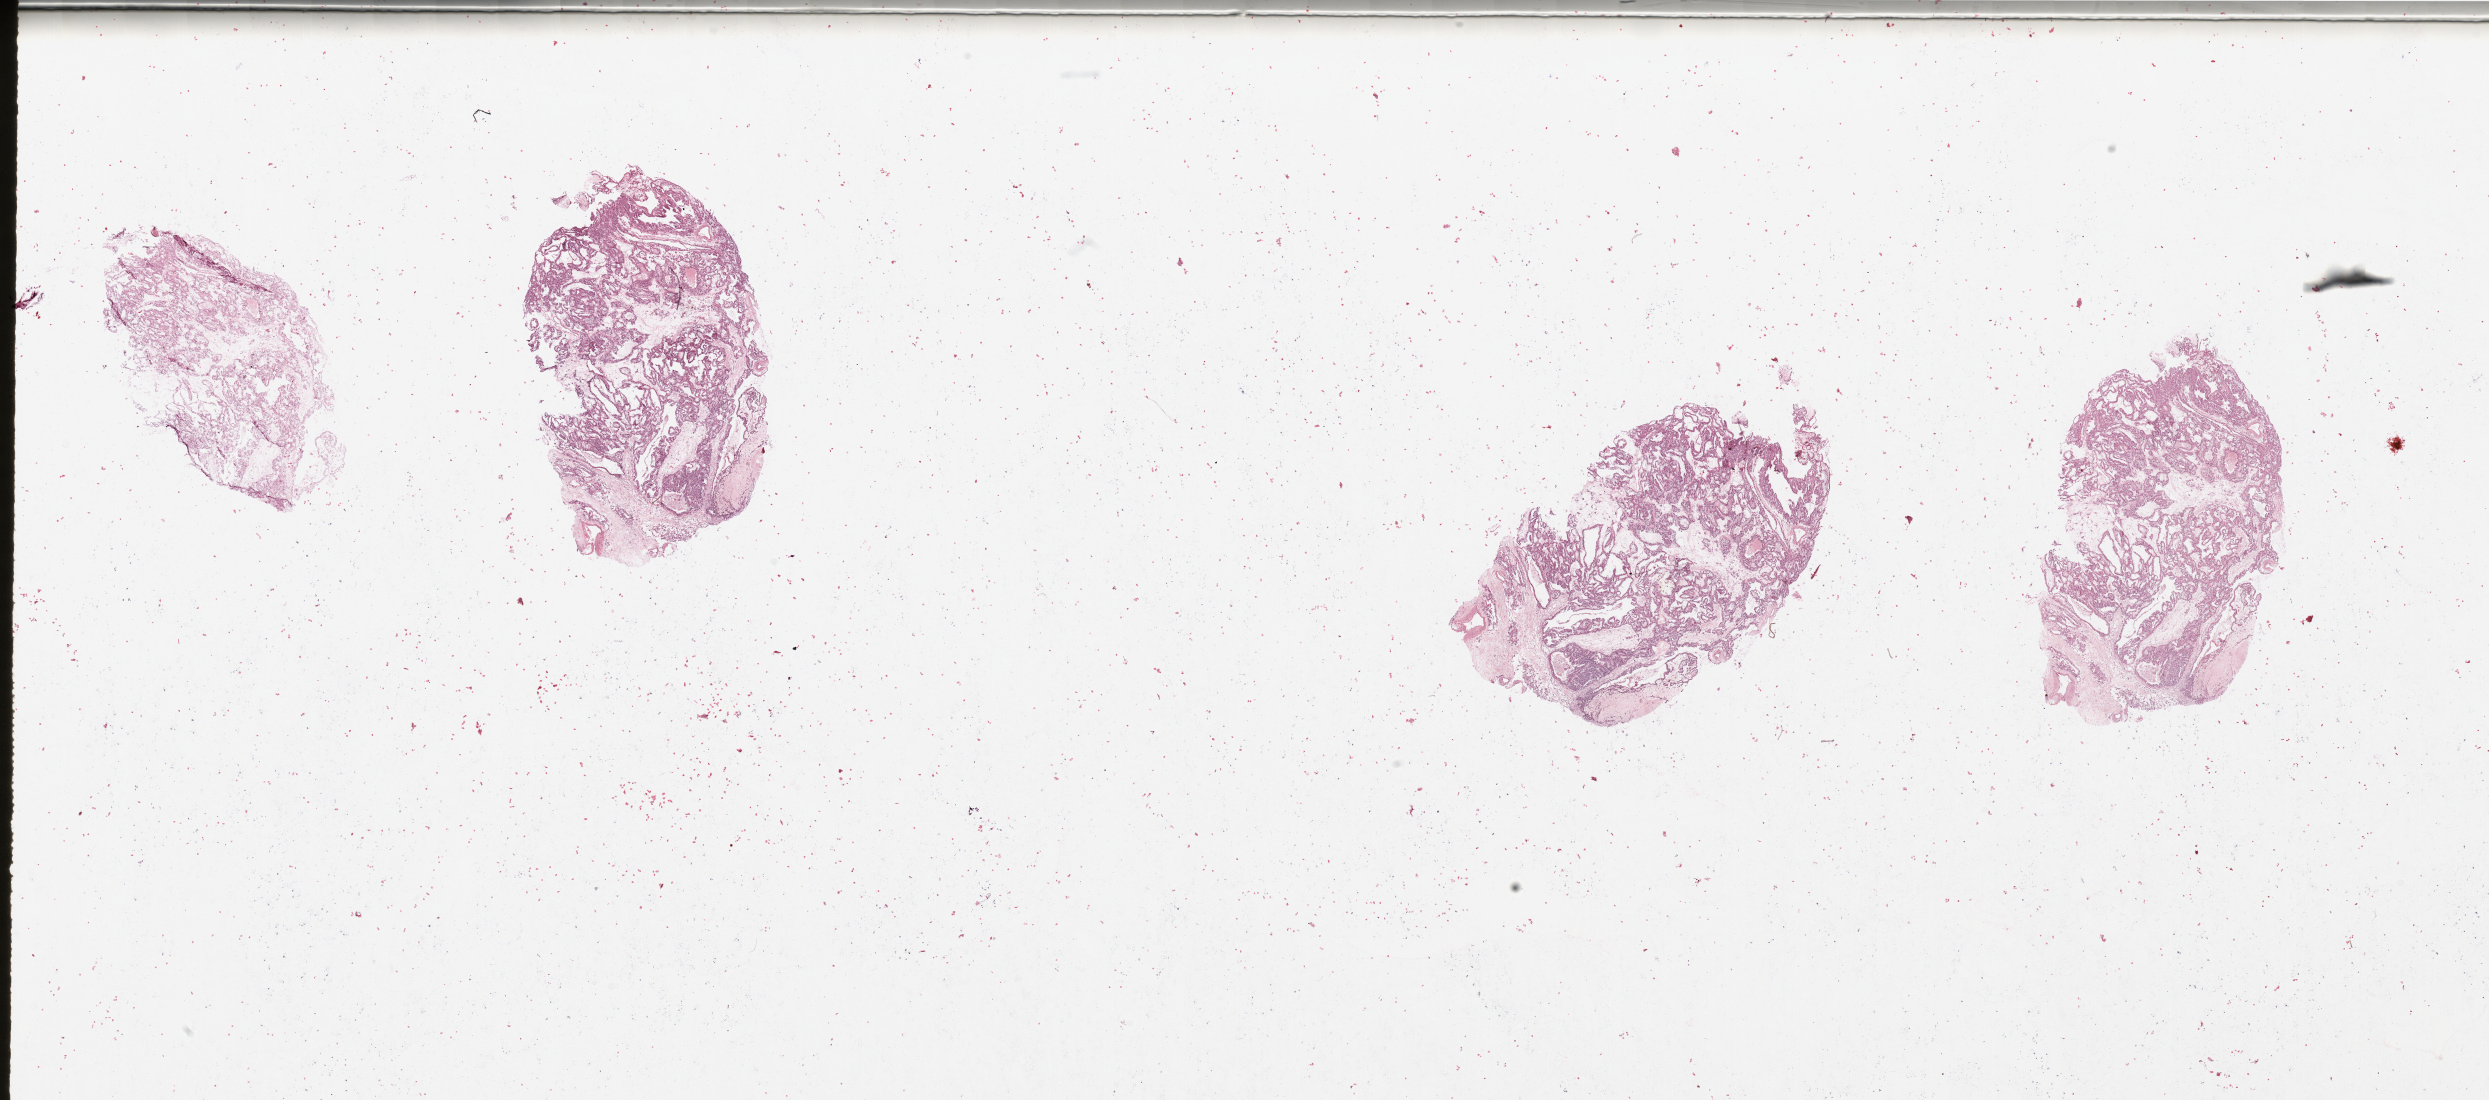
Digitized H&E-stained tissue section (whole slide), whole scanned area (about 39.4 x 17.4 mm) shown as a low-resolution overview. Tumour tissue sample, sampled site: kidney. 46-year-old male patient. Histologic grade: G2 (moderately differentiated). Slide review estimates, as recorded: tumour nuclei 80%, necrosis 0%.
AJCC pathologic stage: I. Diagnosis: Renal cell carcinoma, NOS. Primary tumour site (as recorded): middle.